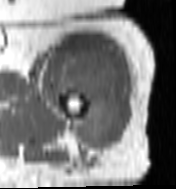
MRI of an extremity soft-tissue mass, one axial slice. Position 84 of 100 along the scan axis. MR volume resampled by the dataset authors to the PET/CT grid (not the native acquisition matrix). 3.27 mm slice thickness. 176 × 189 image matrix, field of view 172 × 185 mm. Female patient. Case-level facts recorded for this patient, not image findings: histological type: undifferentiated – high grade; grade: high; site of the primary tumour: left thigh.
Structures marked on this image (expert contour drawn on MRI and transferred to this co-registered scan by the dataset authors):
- gross tumour volume including surrounding oedema: bounding box (x1, y1, x2, y2) in pixels: (60, 52, 120, 149)
- gross tumour volume (mass): (62, 54, 118, 145)